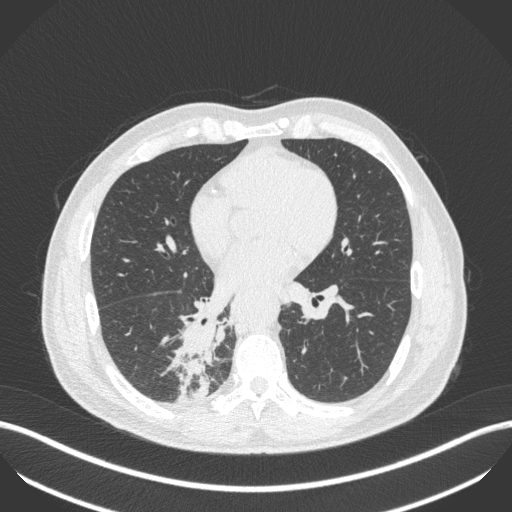
Chest CT, one axial slice; slice 216 of 451 in the series (ordered by position); lung window (W 1500 / L -600 HU); 512 × 512 image matrix, field of view 400 × 400 mm. Male patient, age 61 years. From the clinical record (not read from this slice): clinical TNM (as recorded): T1 N0 M0.
Annotated regions visible in this slice (bounding box drawn by a radiologist):
- lung tumour (recorded histology: small cell carcinoma): box from (x=171, y=318) to (x=228, y=411) px